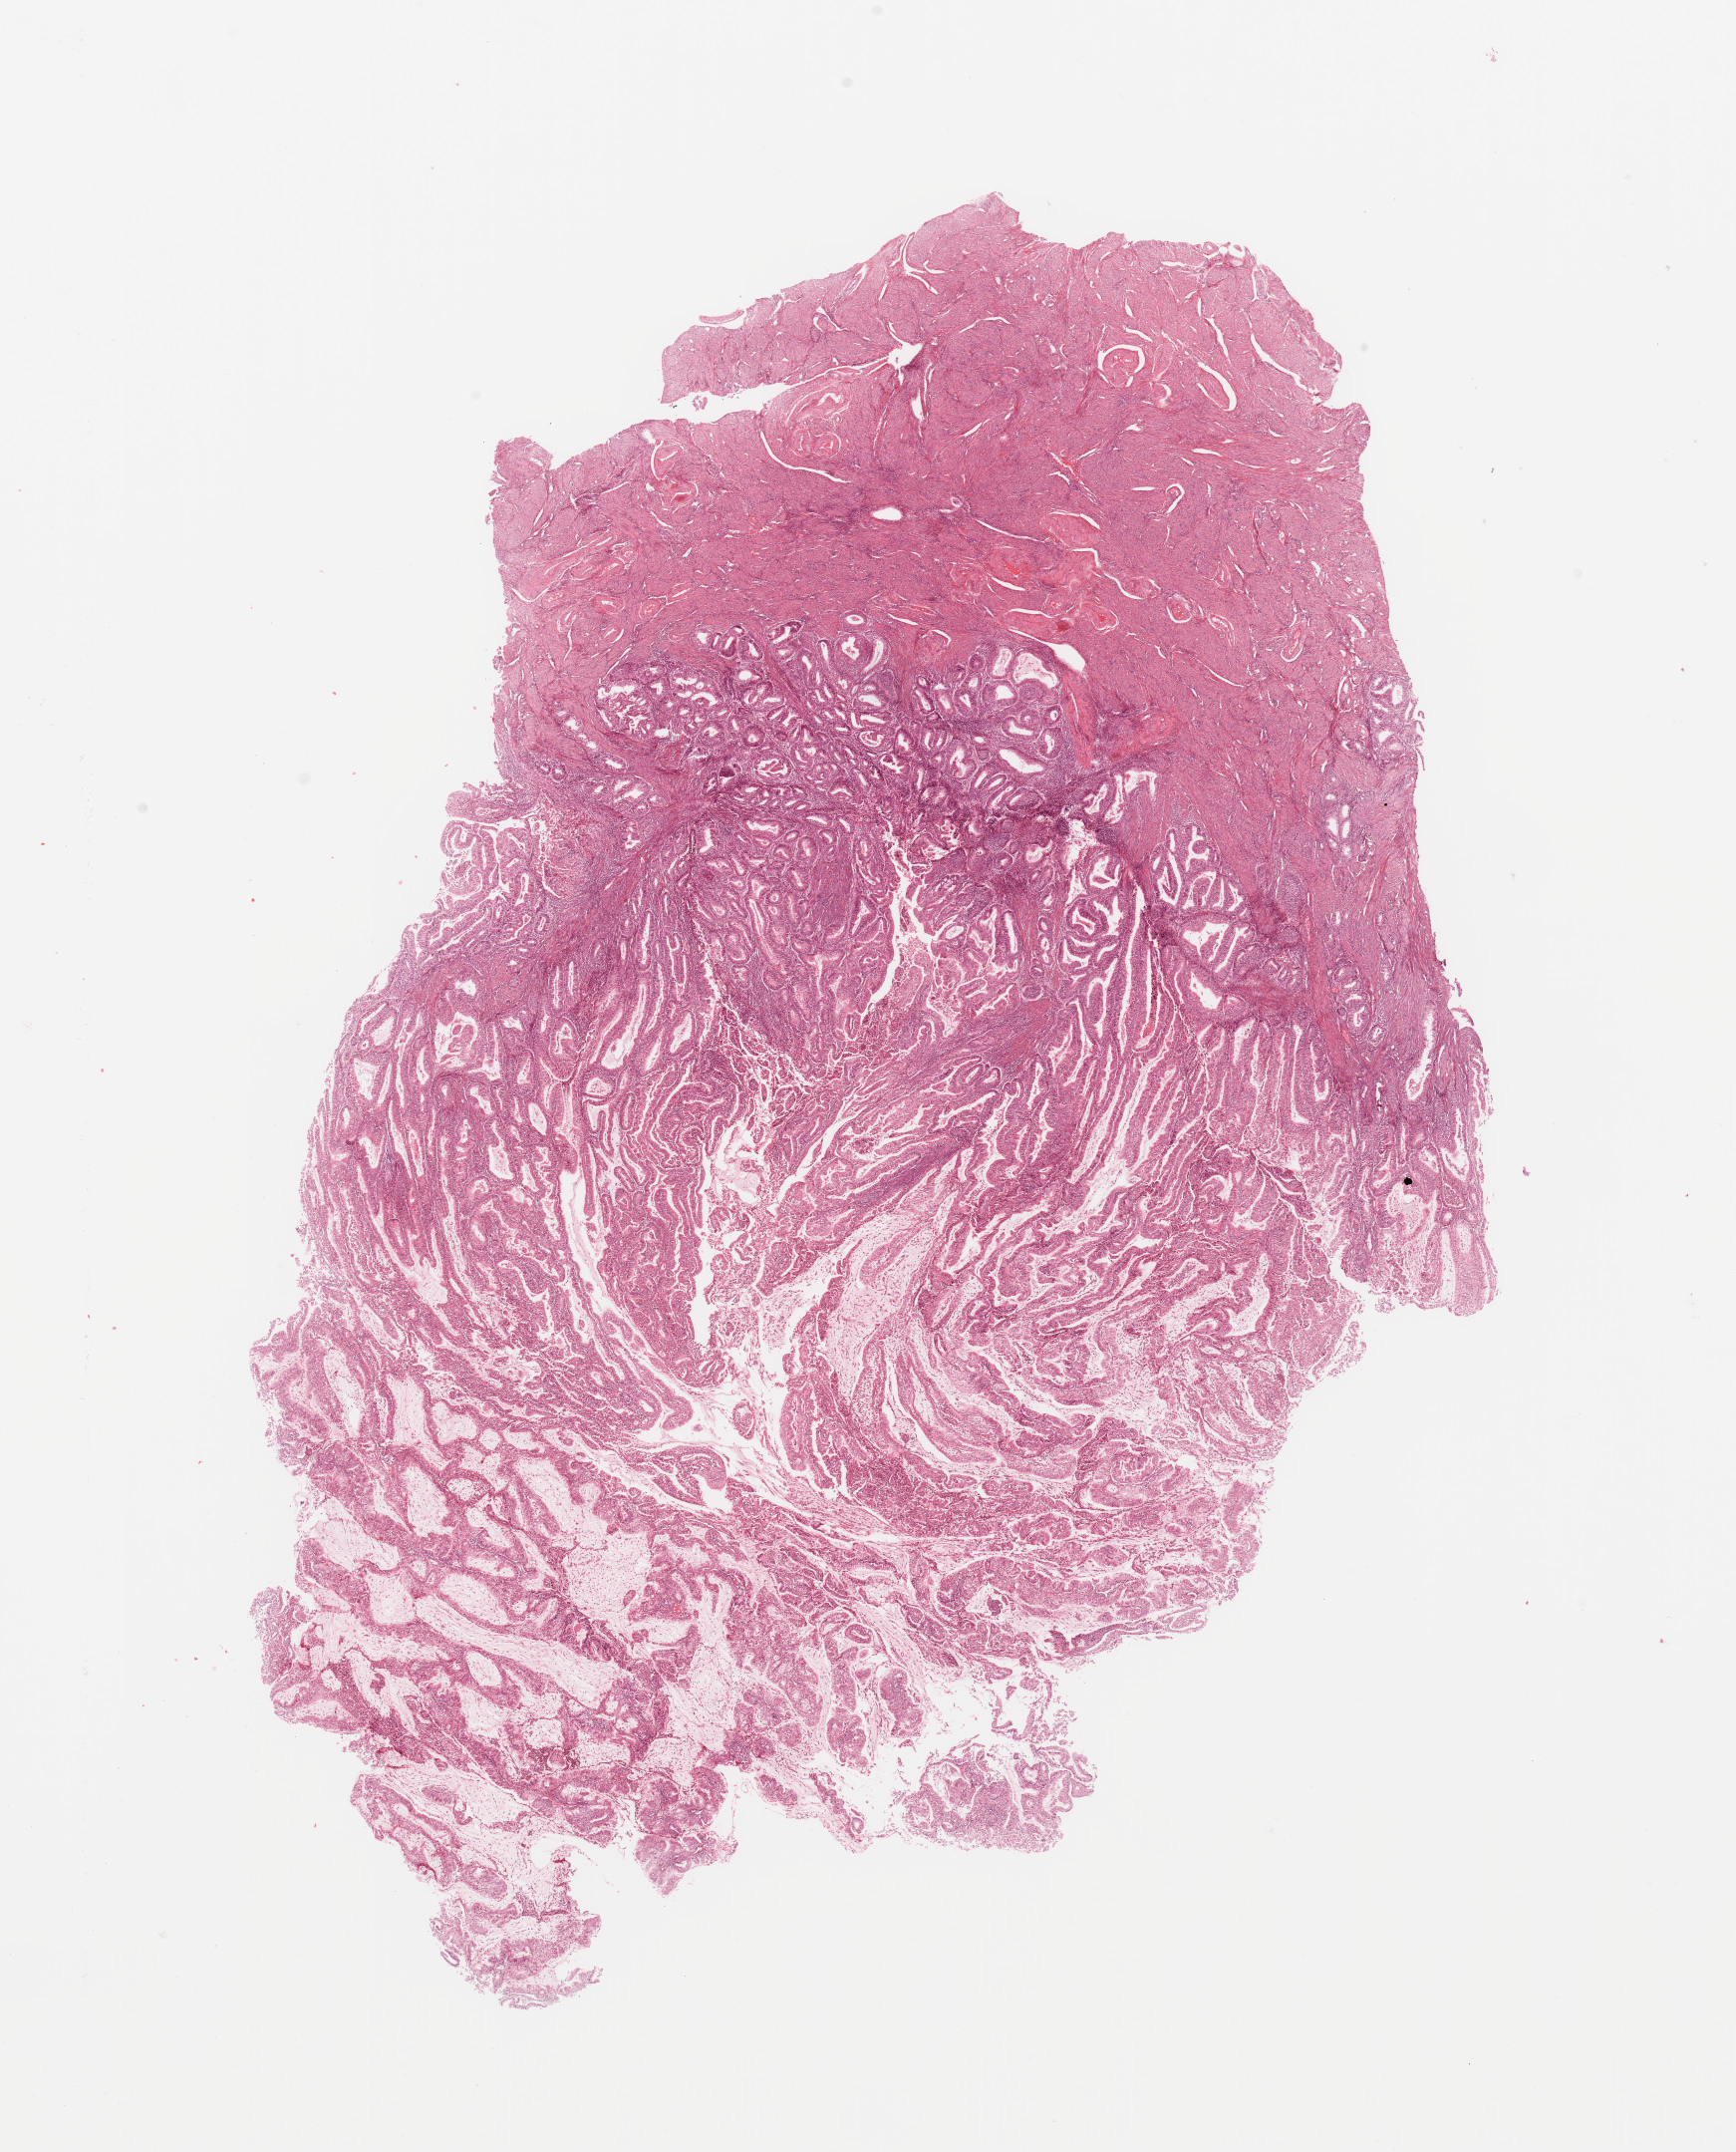
Digitized Hematoxylin and eosin (H&E) stained tissue section (whole slide) — whole scanned area (about 13.8 x 17.1 mm, slide scanned at 20x) shown as a low-resolution overview, tumour tissue sample, sampled site: uterus. Female, 57 y/o. Histologic grade: G1 (well differentiated). Composition of this section per pathologist review: tumour nuclei 80%, necrosis 0%.
- AJCC pathologic stage: I
- diagnosis: Endometrioid adenocarcinoma, NOS